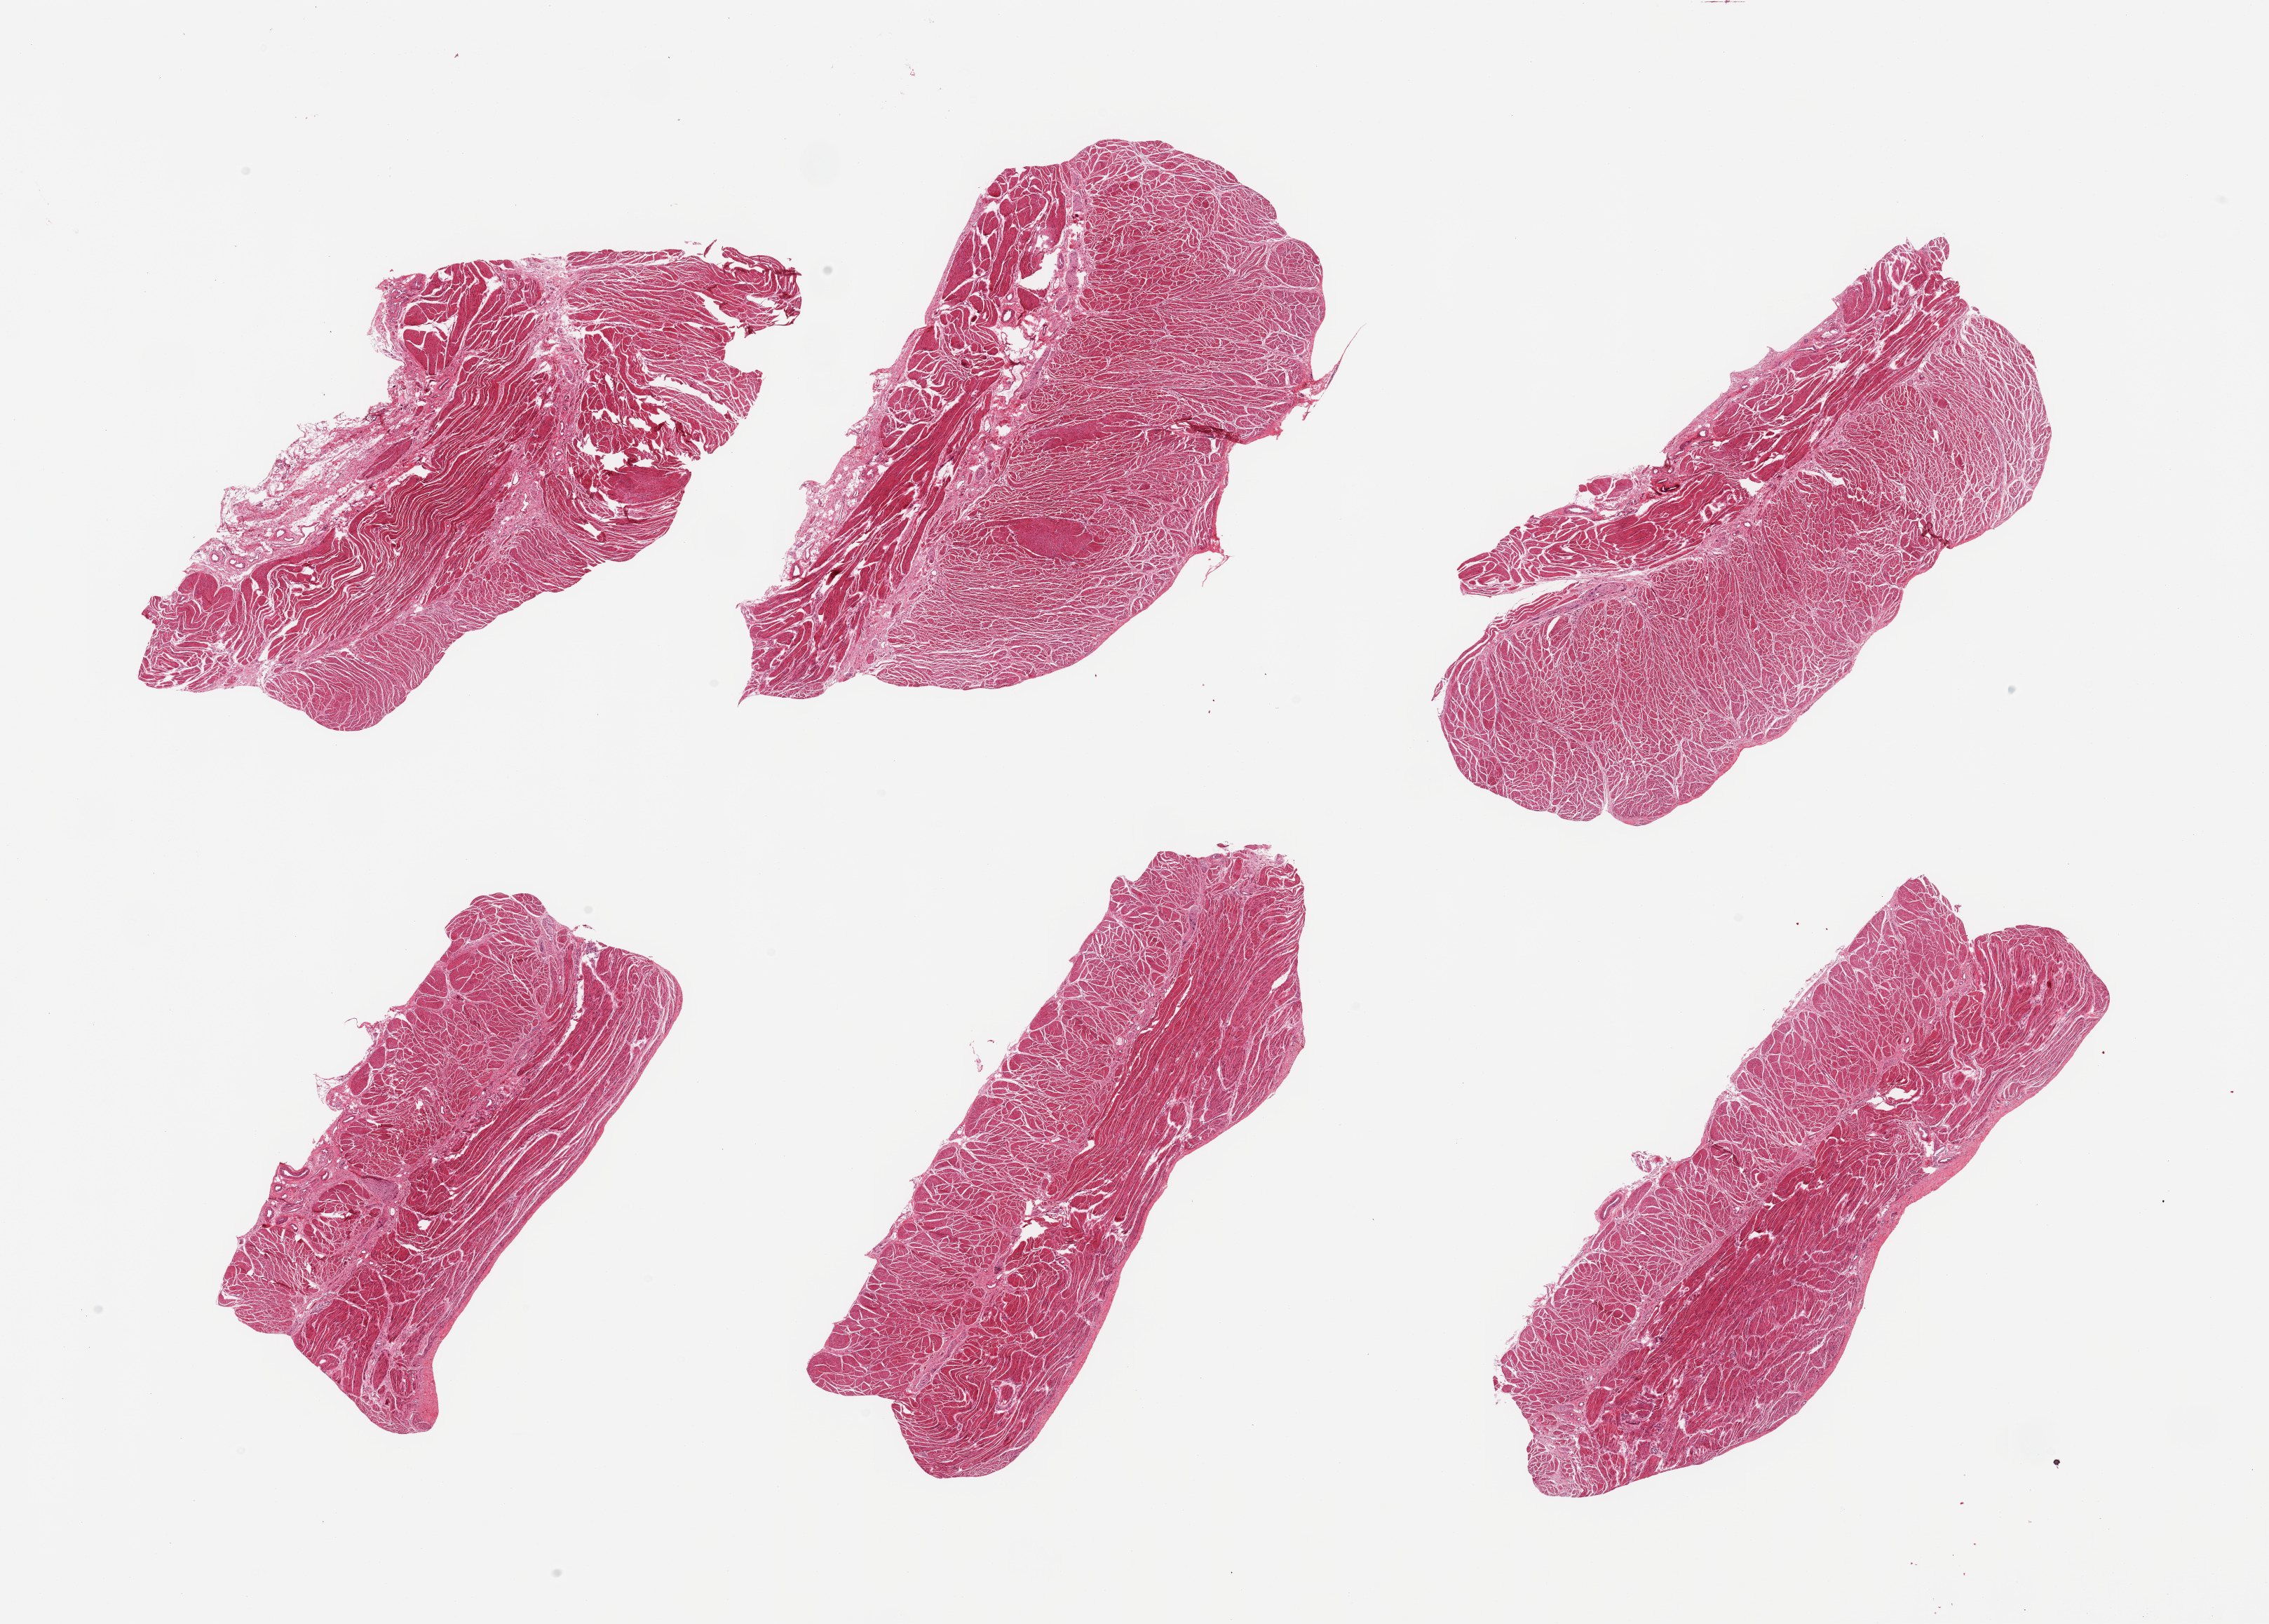
Digitized haematoxylin and eosin-stained section, whole scanned area (about 25.6 x 18.3 mm) shown as a low-resolution overview, PAXgene-fixed paraffin-embedded (PFPE) section, section of gastroesophageal junction (target tissue), donor tissue sample. Male donor.
Pathologist's review note for this sample: 6 pieces, confirmed target muscularis.